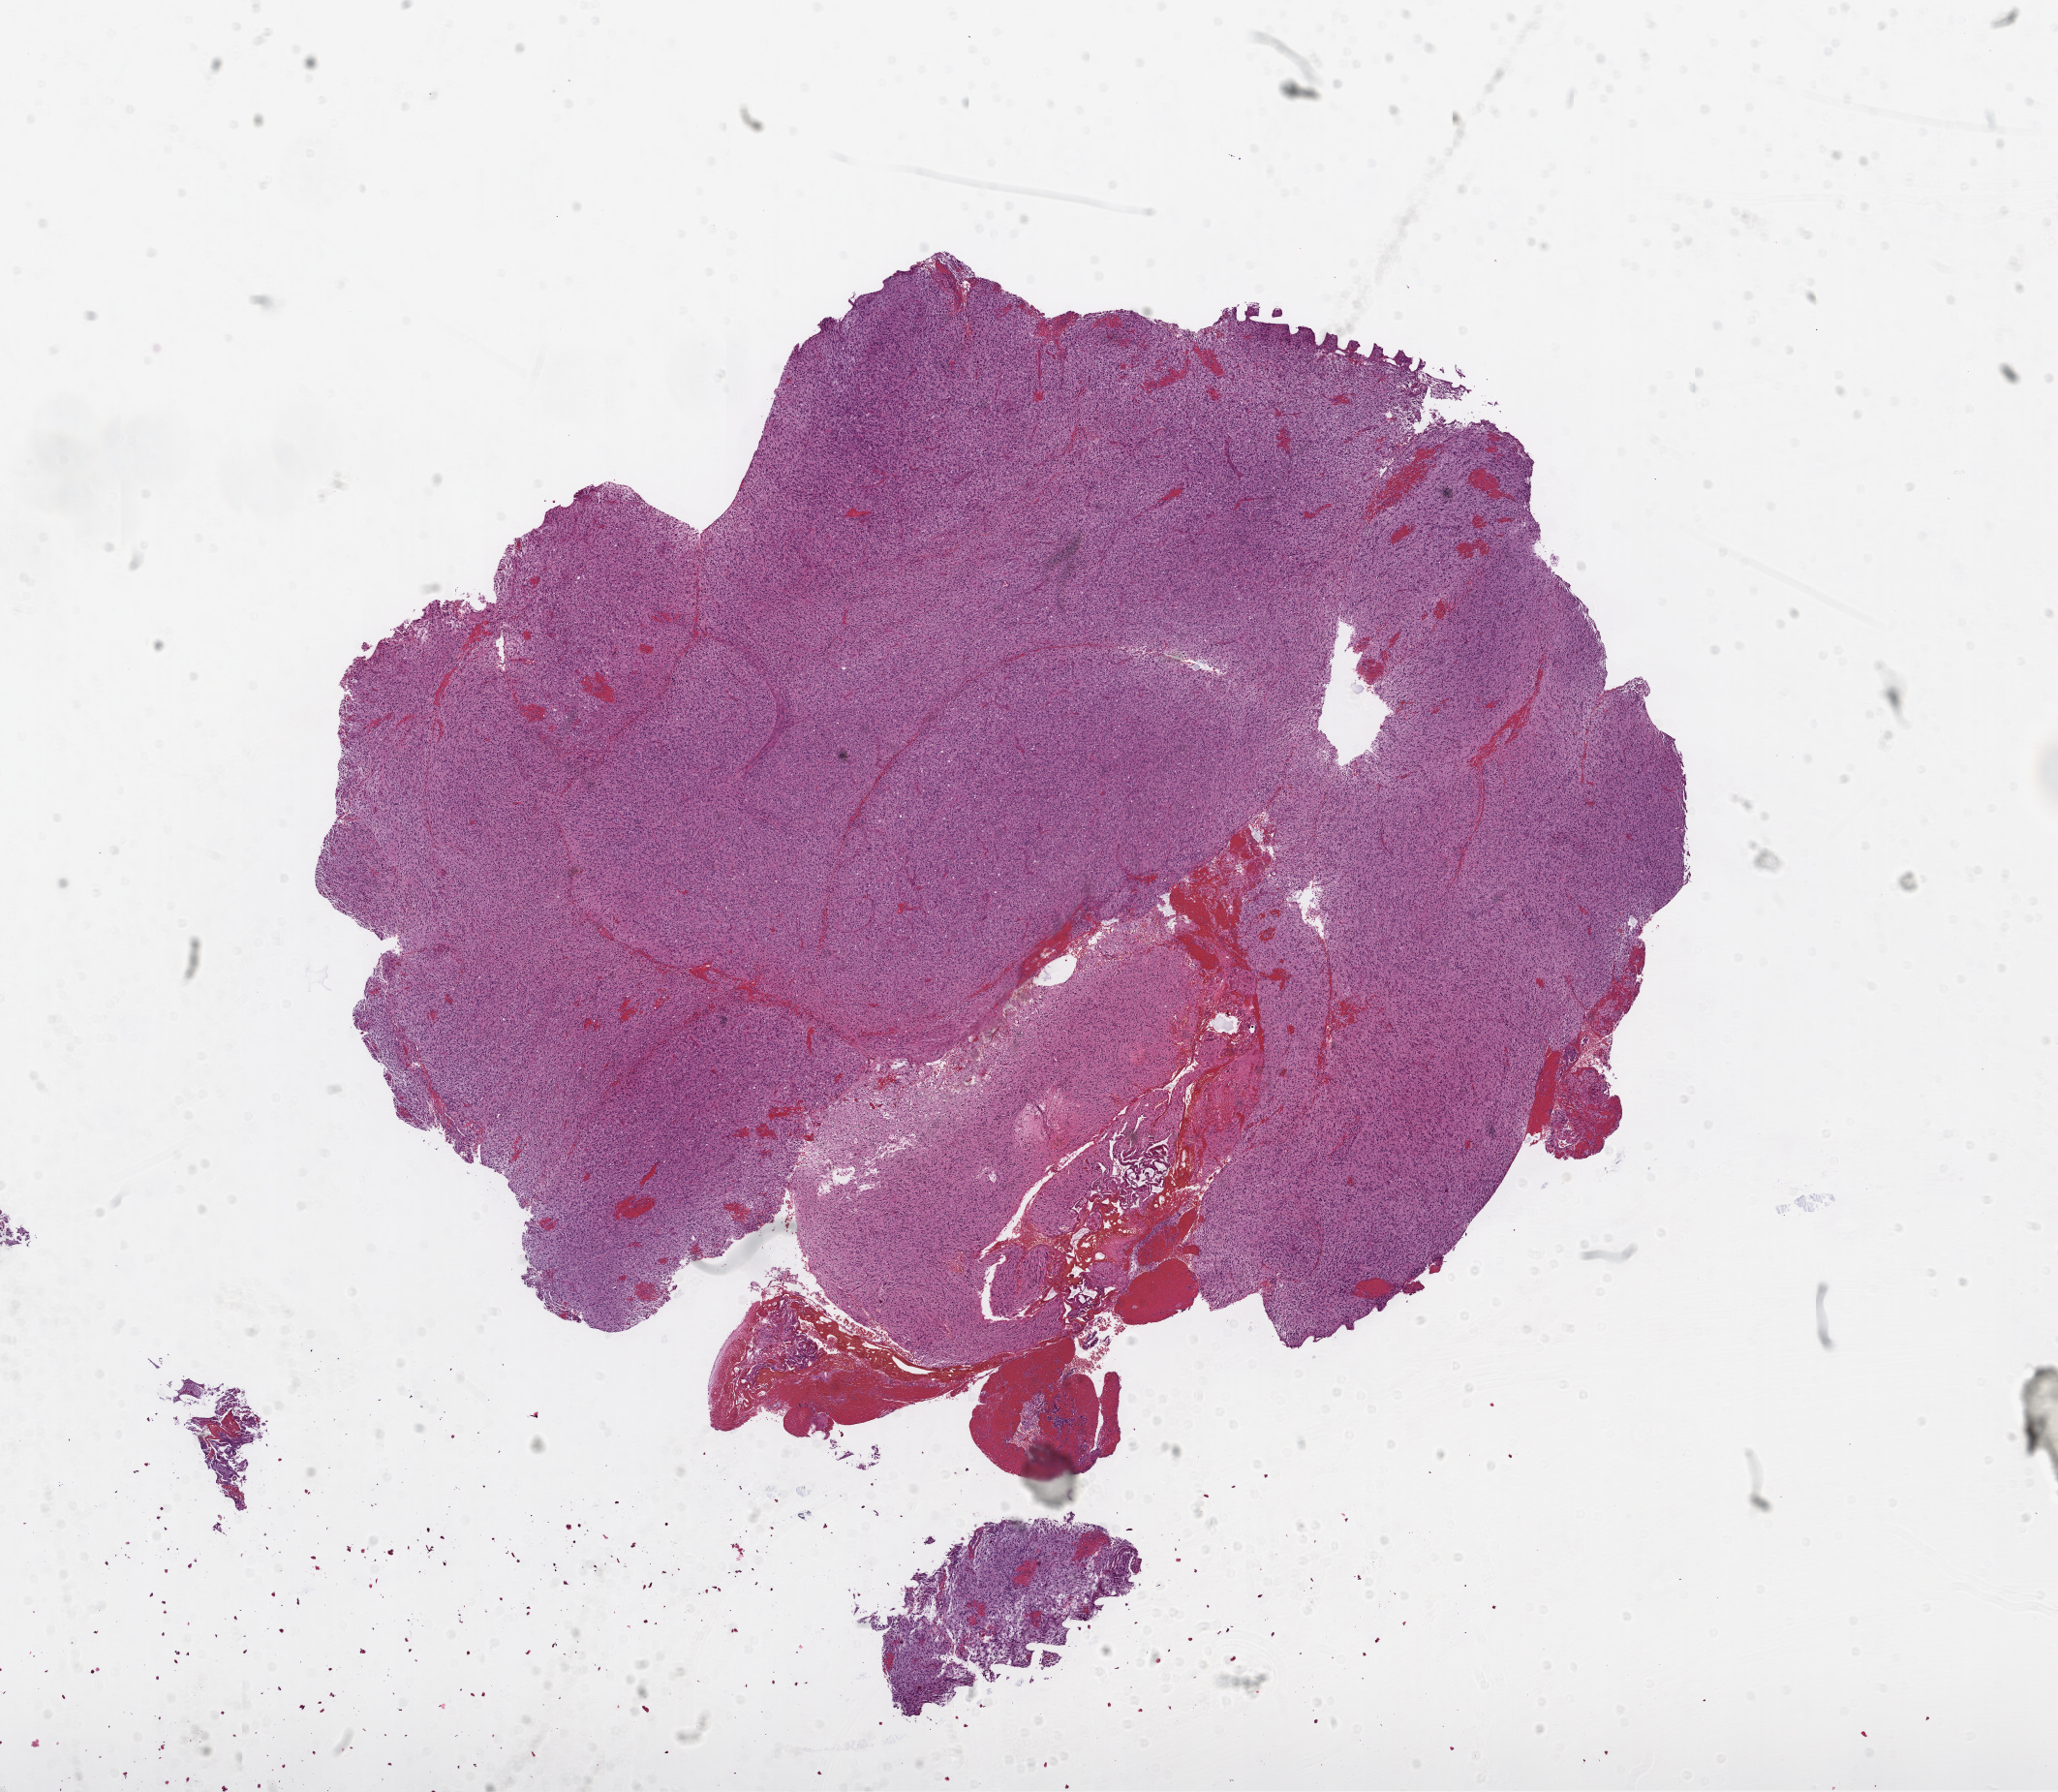
Whole-slide histology image, H&E, a low-resolution overview of the entire scanned area, about 17.1 x 14.8 mm (from a 20x scan), frozen section from the top of the tissue portion, primary tumour sample from the brain. Male patient; age at initial diagnosis 88 years. Slide review estimates, as recorded: tumour cells 99%, tumour nuclei 85%, normal cells 0%, stromal cells 0%, necrosis 1%.
* pathologic diagnosis: Glioblastoma